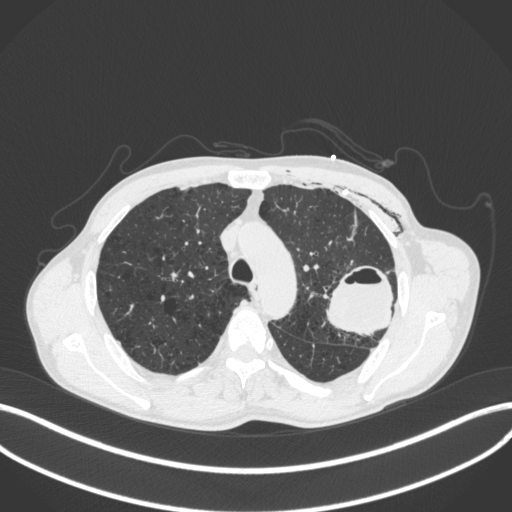
Chest CT, one axial slice; slice 295 of 416 in the series (ordered by position); reconstruction kernel B31f; lung window (W 1500 / L -600 HU); 512 × 512 image matrix, field of view 400 × 400 mm. Male patient, age 58 years. Case-level facts recorded for this patient, not image findings: clinical TNM (as recorded): T3 N0 M0.
Structures marked on this image (rectangle marked by the reading radiologist):
- lung tumour (recorded histology: adenocarcinoma): bounding box <325,260,396,339> (left, top, right, bottom; pixels)